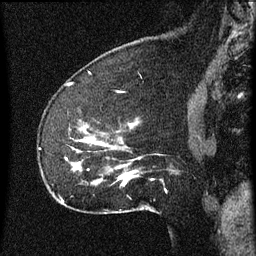
Breast MRI (dynamic contrast-enhanced), one sagittal slice. Slice 17 of 60 in the series (ordered by position). Dynamic contrast-enhanced series, image 2 of 3 at this slice position (ordered by acquisition). 1.5 T. TE 4.2 ms, TR 8 ms. 2 mm slice thickness. 256 × 256 image matrix, field of view 180 × 180 mm. Female patient, age 52 years.
Outlined on this slice (semi-automatic segmentation, software-assisted and operator-edited):
- analysis volume of interest (the breast-tissue region the enhancement analysis was run in; not a lesion): box from (x=54, y=120) to (x=167, y=207) px
- tumour enhancement mask (voxels above the 70 % enhancement threshold inside the analysis volume of interest): (x=77, y=138)–(x=131, y=185)